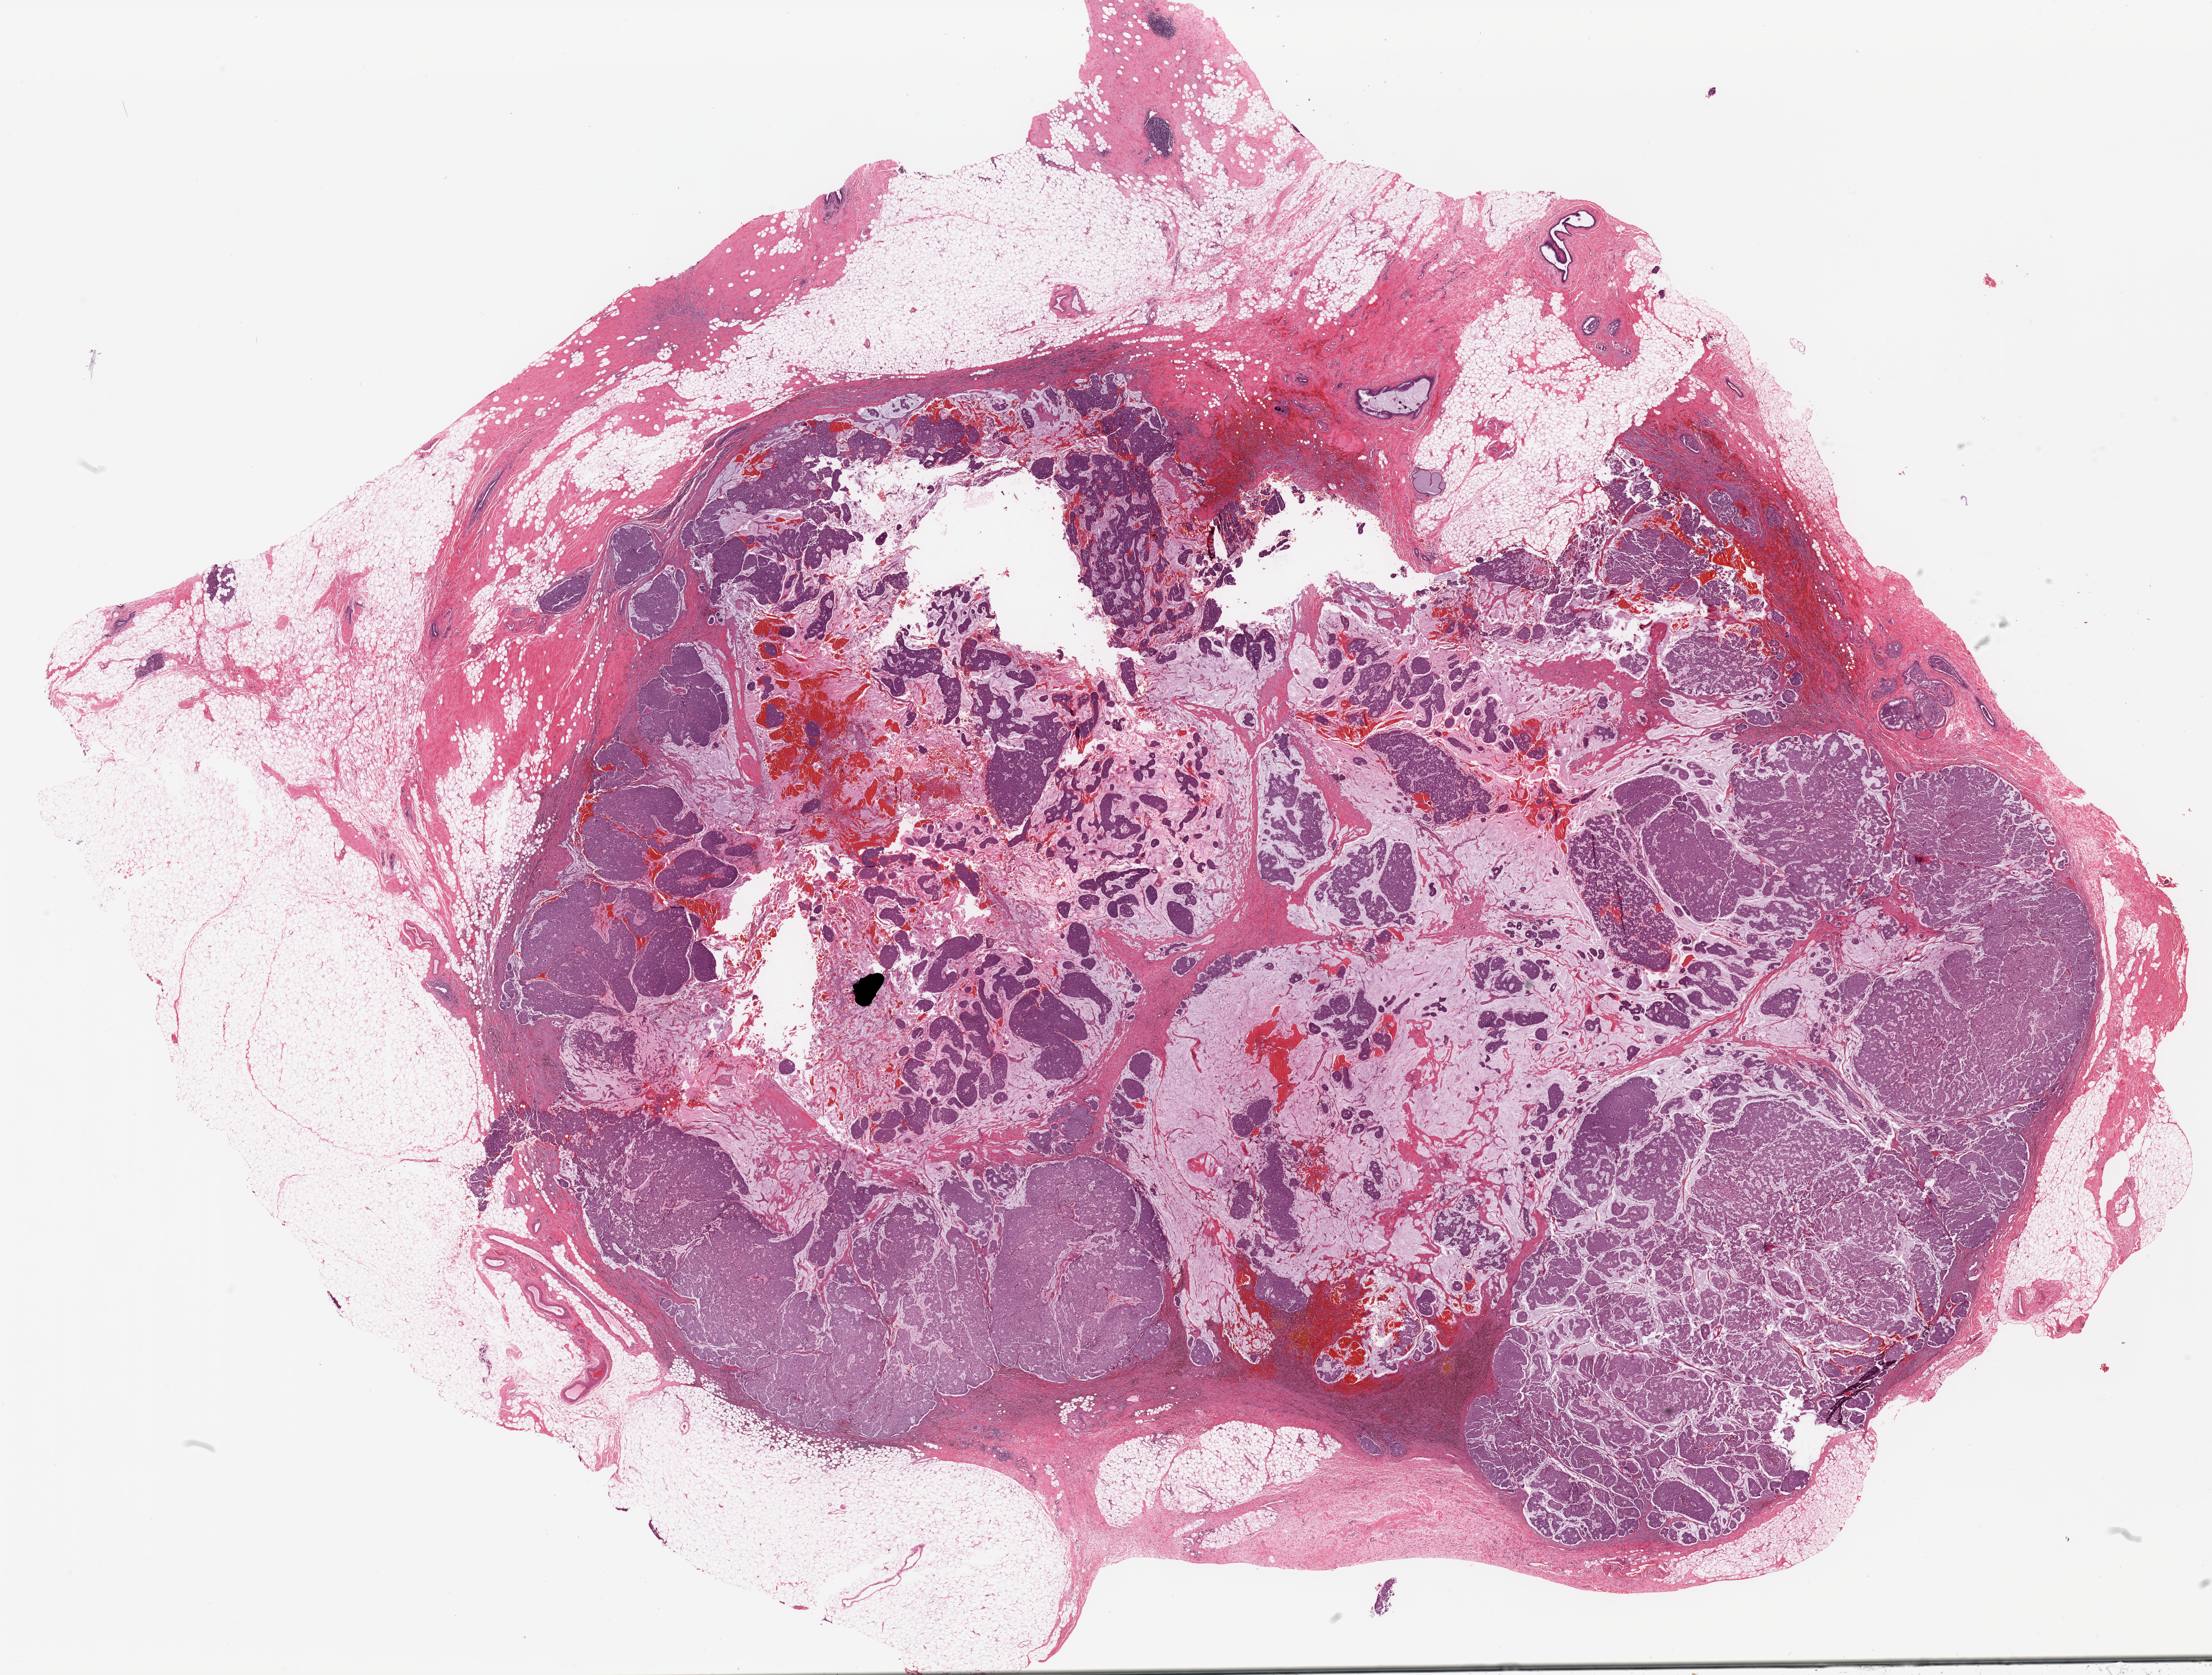
Digitized H&E tissue section (whole slide) — shown as a low-resolution overview of the whole scanned area (about 30.8 x 23.3 mm, slide scanned at 20x), formalin-fixed paraffin-embedded (FFPE) diagnostic section, primary tumour sample from the breast. Patient: female, age at initial diagnosis 69 years.
Histologic diagnosis: Infiltrating duct mixed with other types of carcinoma.